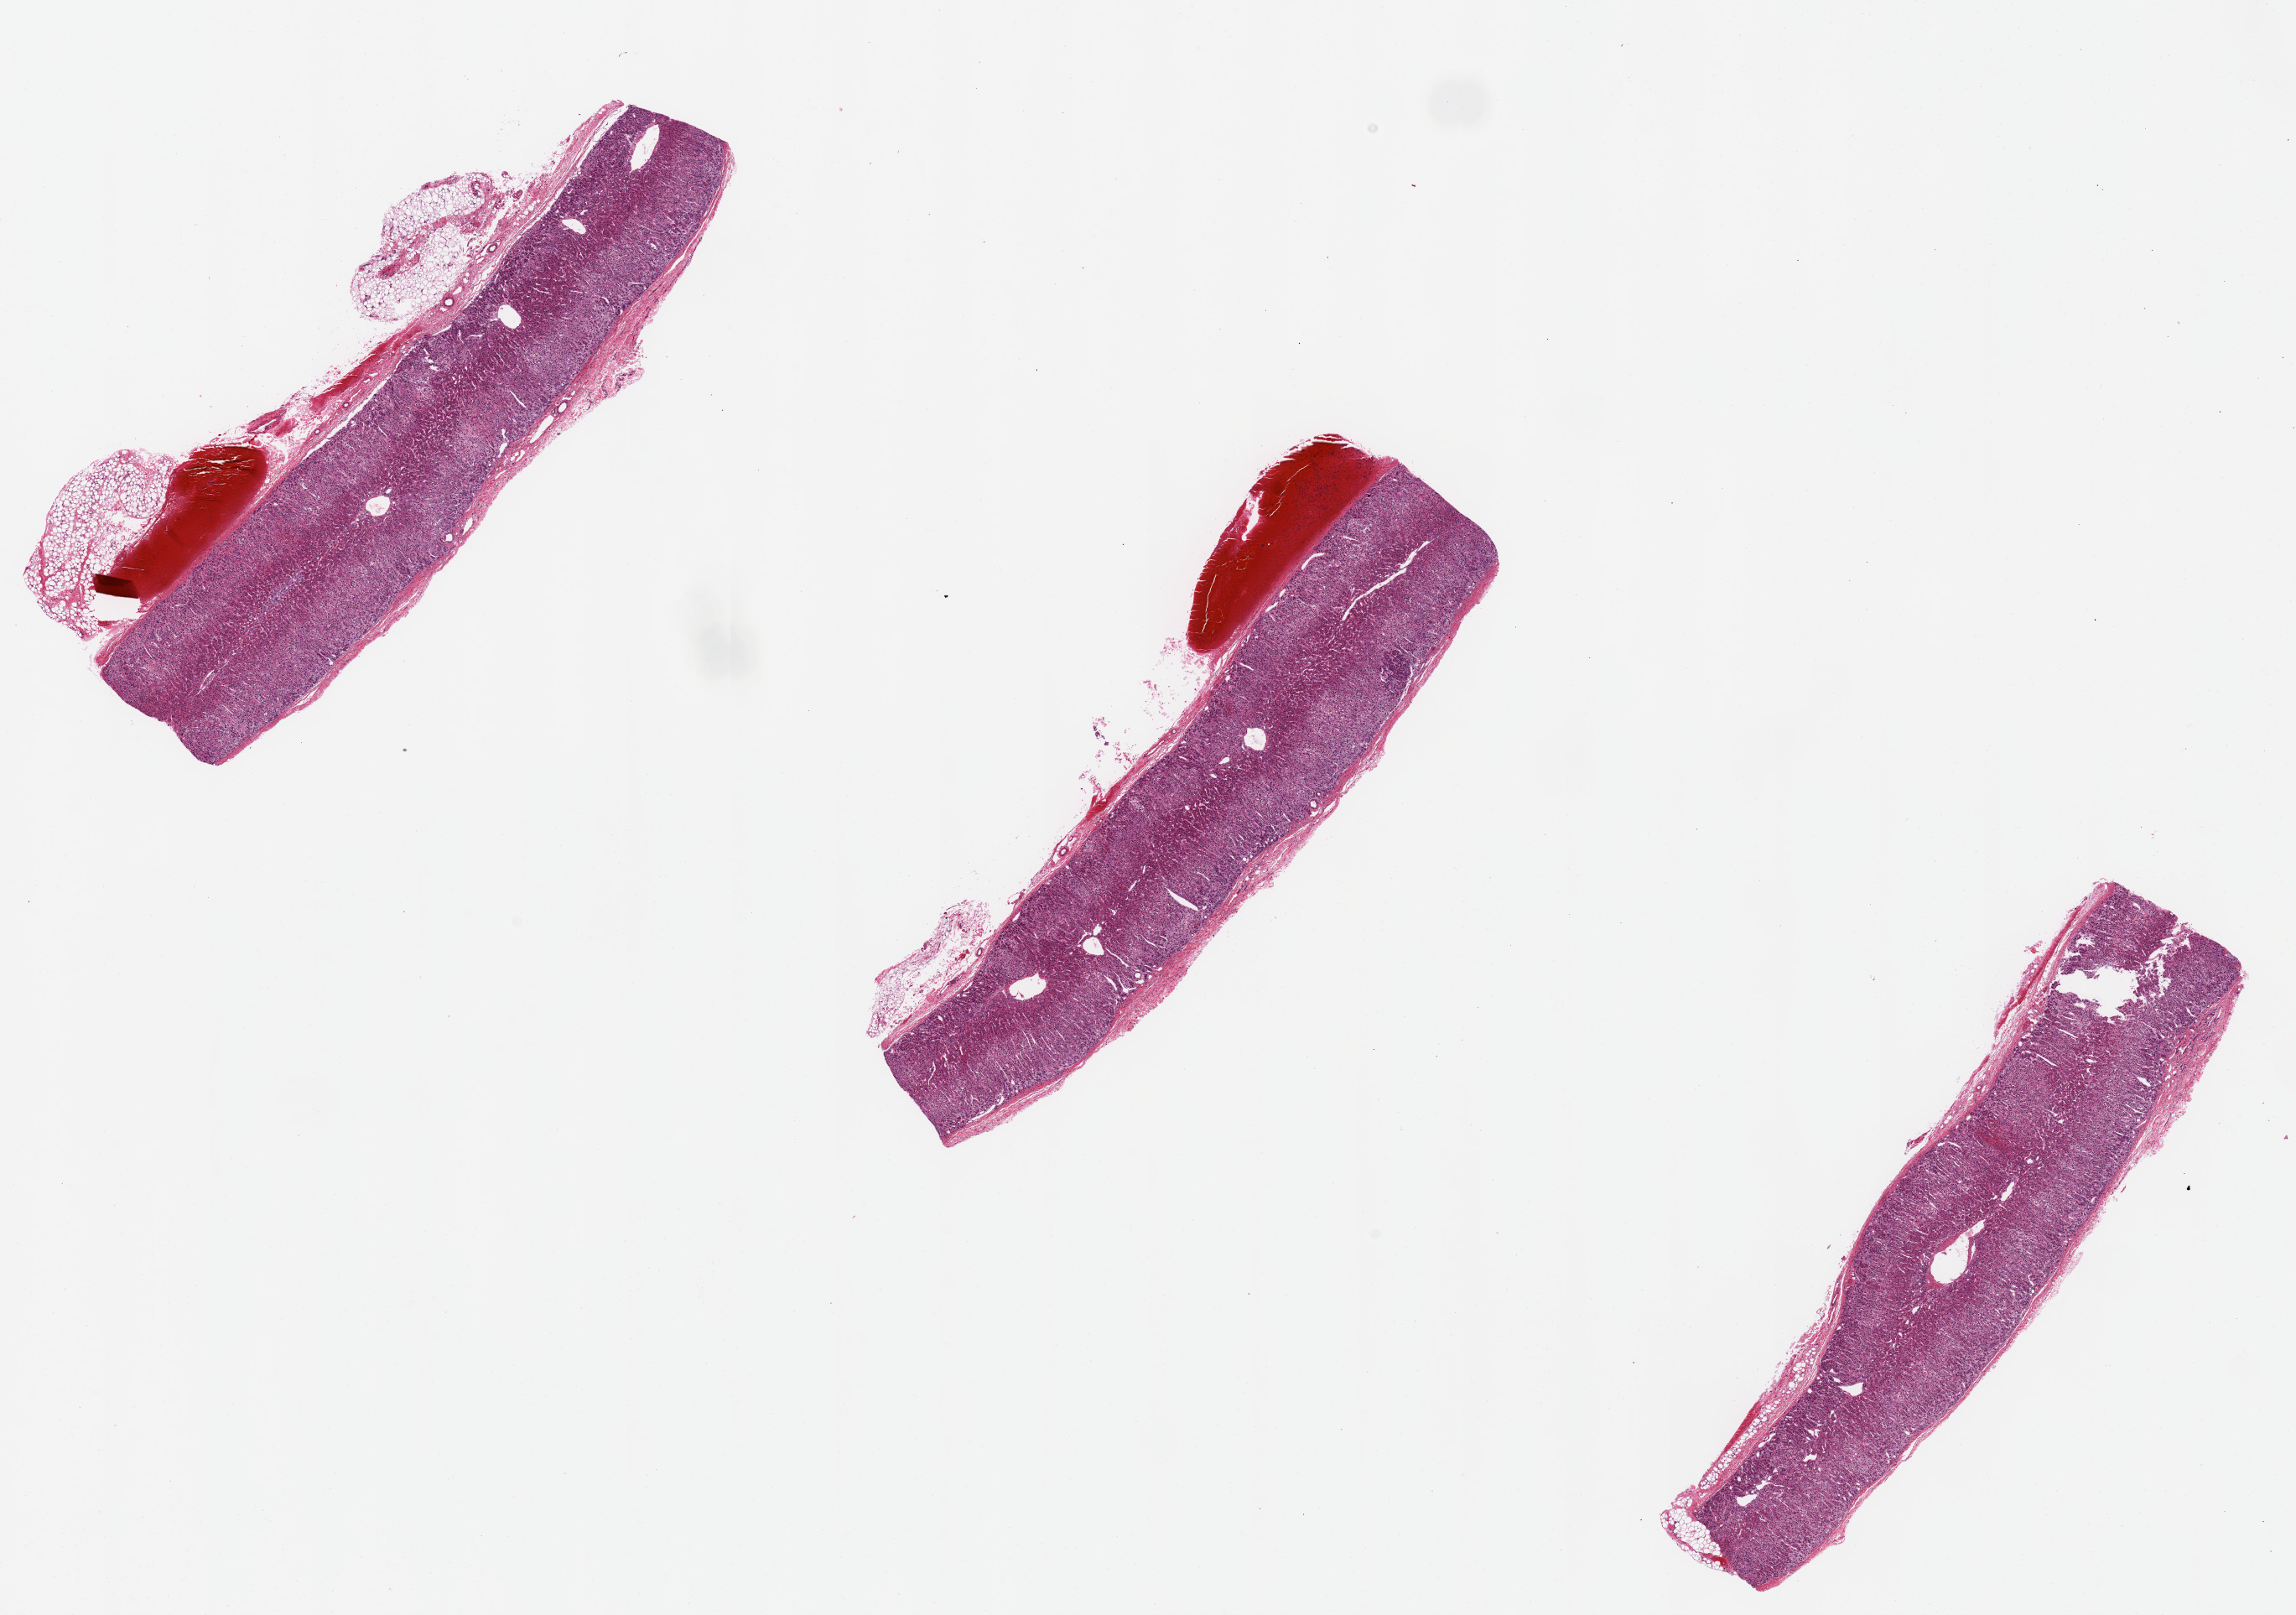
Digitized hematoxylin and eosin (H&E)-stained section — low-resolution overview of the scanned area, about 21.7 x 15.2 mm (slide scanned at 20x), PAXgene-fixed paraffin-embedded (PFPE) section, section of adrenal gland (target tissue), donor tissue sample. Male donor.
Reviewer comment on this tissue sample: 3 pieces; cortex, well preserved.